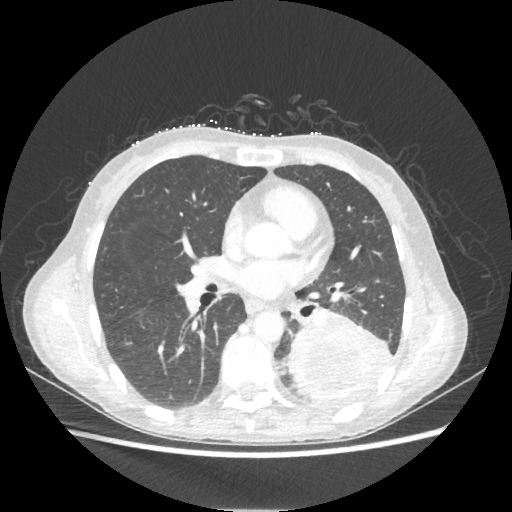
Chest CT, one axial slice. Lung window (W 1500 / L -600 HU). 512 × 512 image matrix, field of view 360 × 360 mm. Female patient, age 53 years. From the clinical record (not read from this slice): clinical TNM (as recorded): T3 N0 M0.
Structures marked on this image (rectangle marked by the reading radiologist):
- lung tumour (recorded histology: adenocarcinoma): box from (x=286, y=309) to (x=394, y=402) px